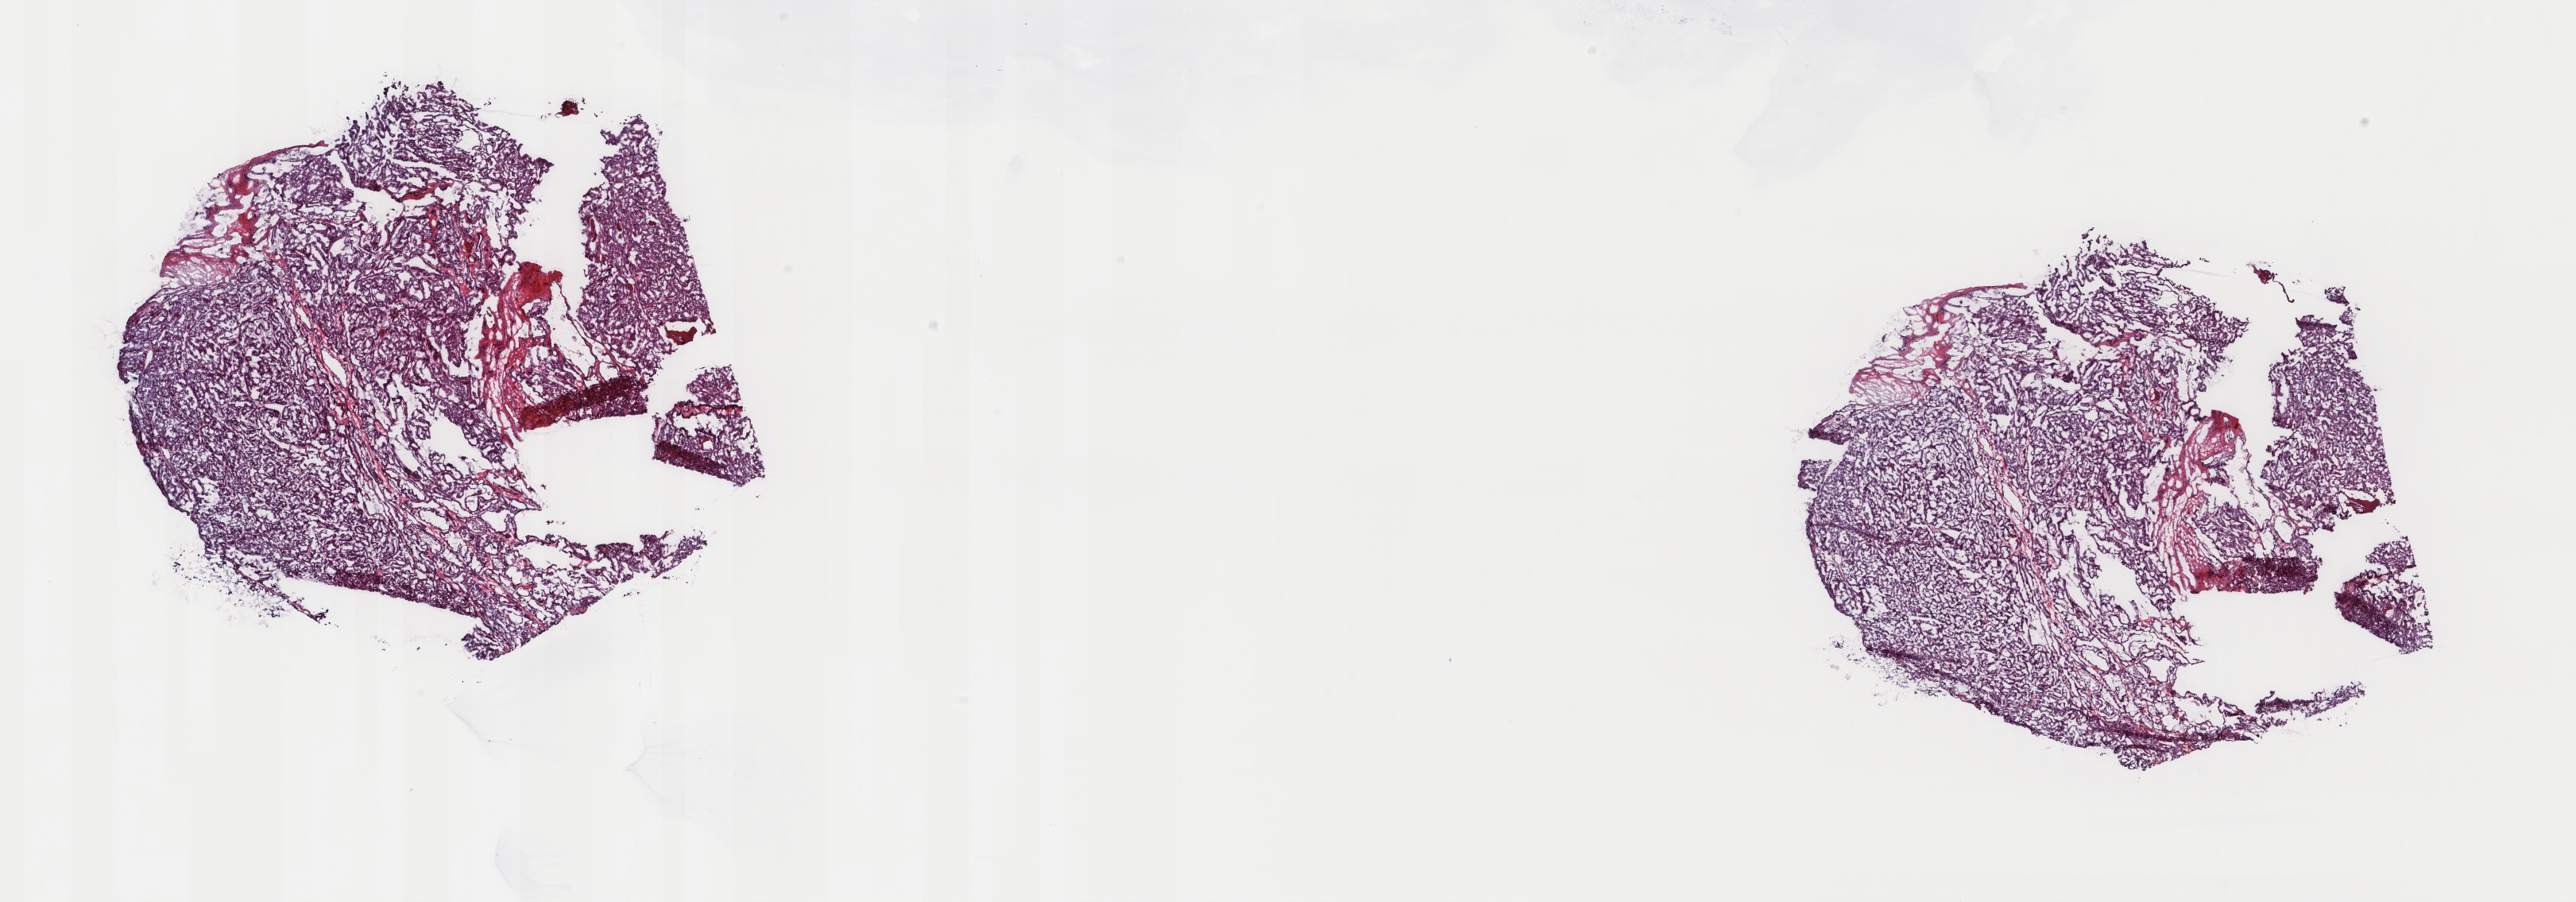
H&E-stained whole-slide image — a low-resolution overview of the entire scanned area, about 25.7 x 9.0 mm. Frozen section. Sample: primary tumour, thyroid. Patient: female, age at initial diagnosis 37 years. Pathologist review of this section (percent, as recorded): tumour cells 90%, tumour nuclei 90%.
Pathologic diagnosis: Papillary adenocarcinoma, NOS (thyroid gland).